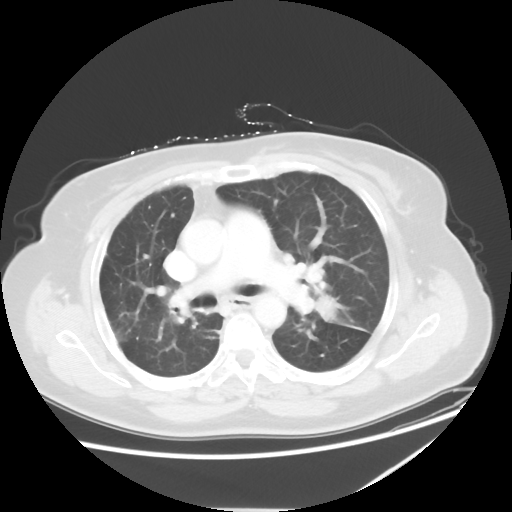
Chest CT, one axial slice; position 34 of 54 along the scan axis; lung window (W 1500 / L -600 HU); 5 mm slice thickness; 512 × 512 image matrix, field of view 384 × 384 mm. Patient: female, 61 years. Case-level facts recorded for this patient, not image findings: clinical TNM (as recorded): T1c N3 M1.
Structures marked on this image (bounding box drawn by a radiologist):
- lung tumour (recorded histology: adenocarcinoma): bounding box <311,291,373,336> (left, top, right, bottom; pixels)